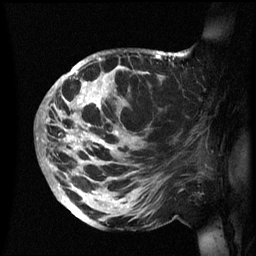
Breast MRI (dynamic contrast-enhanced), one sagittal slice; slice 35 of 60 in the series (ordered by position); dynamic contrast-enhanced series, image 2 of 3 at this slice position (ordered by acquisition); 1.5 T; TE 4.2 ms, TR 8.4 ms; 2.4 mm slice thickness; 256 × 256 image matrix, field of view 230 × 230 mm. Patient: female, 48 years.
Structures marked on this image (semi-automatic segmentation, software-assisted and operator-edited):
- analysis volume of interest (the breast-tissue region the enhancement analysis was run in; not a lesion): bounding box <42,50,191,231> (left, top, right, bottom; pixels)
- tumour enhancement mask (voxels above the 70 % enhancement threshold inside the analysis volume of interest): <42,53,179,217>